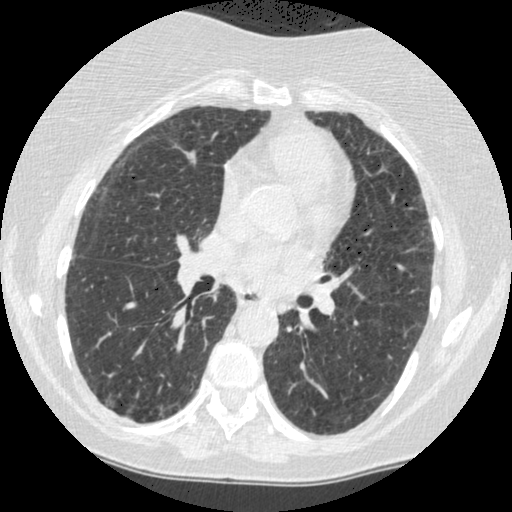
Chest CT (low-dose screening protocol), one axial image, baseline screening round, lung window (W 1500 / L -600 HU). Female participant, aged 60 years at enrolment.
Expert reader's lesion annotation, box from (x=260, y=286) to (x=305, y=328) px. The screening reader recorded 2 non-calcified nodules or masses ≥4 mm on this exam (right lower lobe, left lower lobe); which of them this box marks is not recorded. Official screen result: positive, change unspecified: nodule(s) >= 4 mm or enlarging nodule(s), mass(es), or other non-specific abnormalities suspicious for lung cancer. Participant outcome: lung cancer diagnosed 794 days after this screen (after the third annual screen) — small cell carcinoma, NOS, left lower lobe, undifferentiated (G4), stage IV (AJCC 6th edition), 69 mm at pathology.